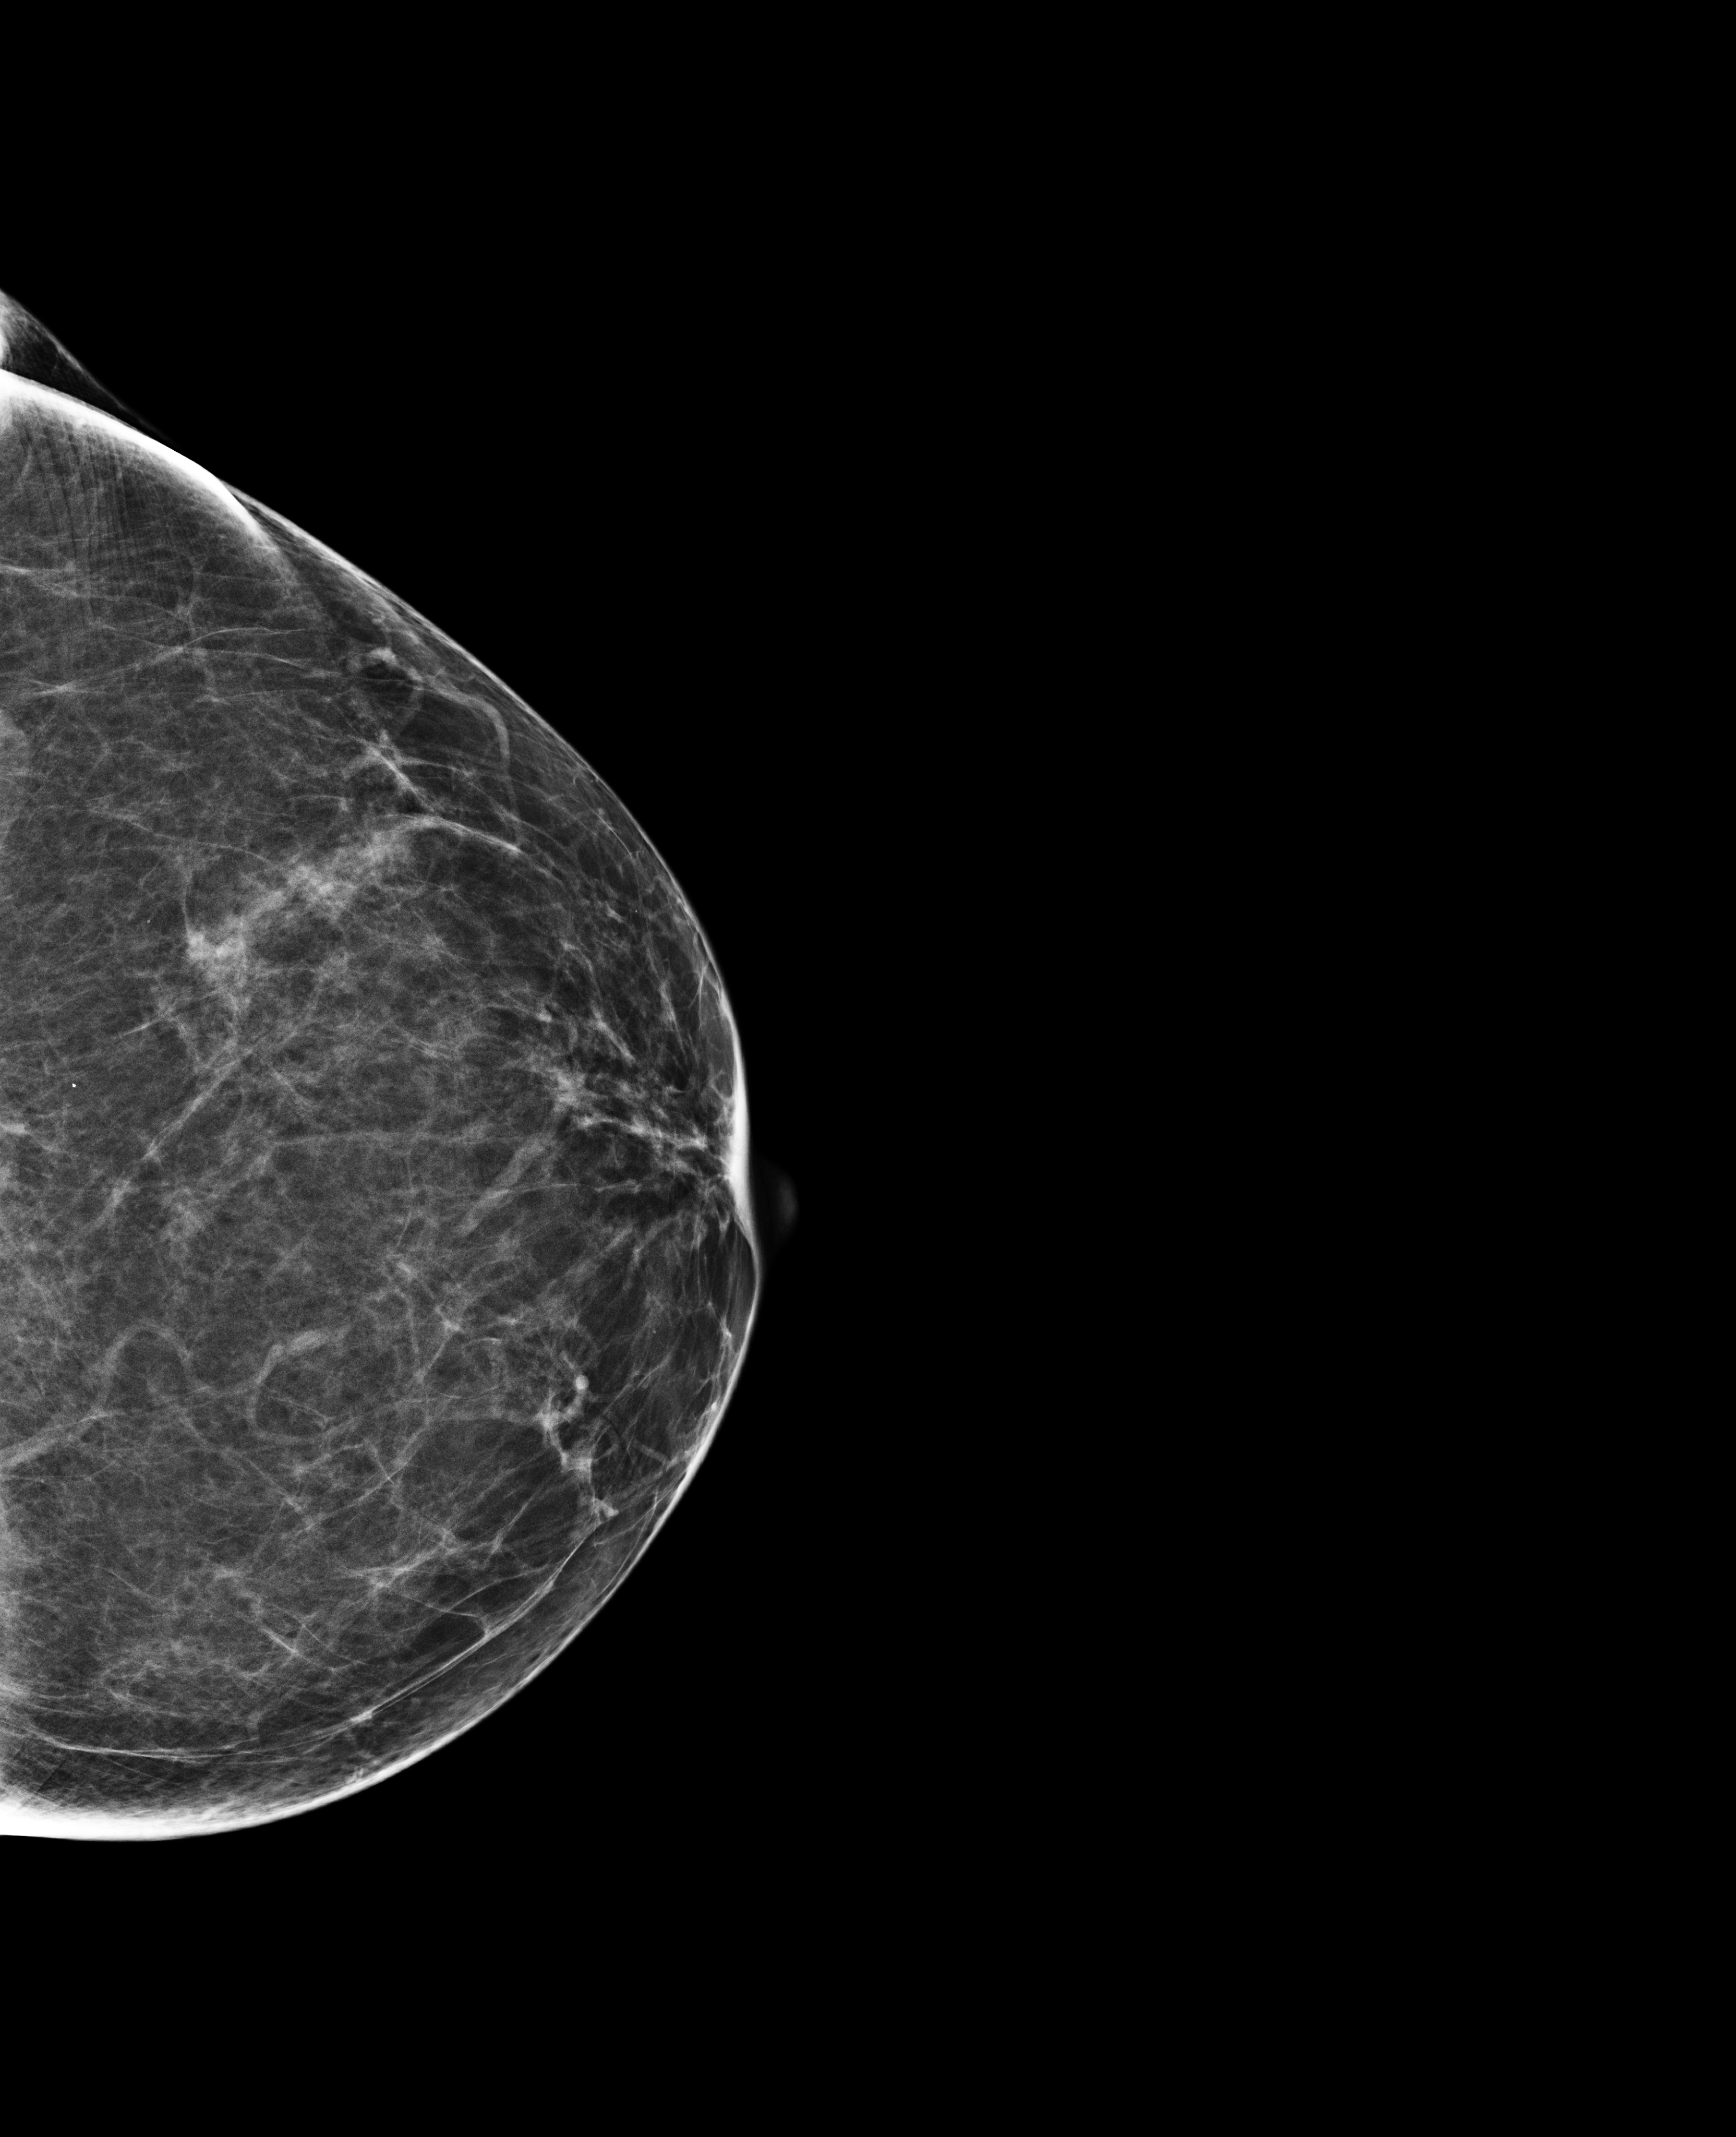
Full-field digital mammogram (FFDM); left breast; CC view; screening examination. Female patient, age 54 years.
- breast density at the screening exam (both breasts): heterogeneously dense (BI-RADS density category c)
- final BI-RADS category for the screening round (tomosynthesis exam, both breasts): category 2
- recall: recalled for additional imaging after this screen